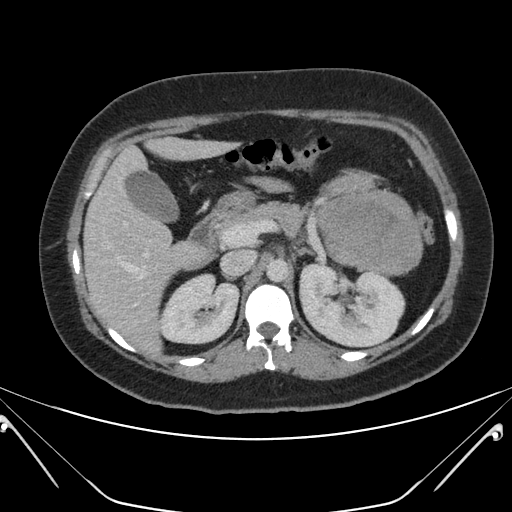
Contrast-enhanced abdominal CT, one axial slice. Intravenous contrast given. Soft-tissue window (W 400 / L 40 HU). 3 mm slice thickness. 512 × 512 image matrix, field of view 394 × 394 mm. Female patient, age 26 years. From the clinical record (not read from this slice): diagnosis: adrenocortical carcinoma; tumour side: left adrenal; tumour size at pathology: 28 cm.
Structures marked on this image (semi-automatic segmentation, software-assisted and operator-edited):
- mass: bounding box [x1, y1, x2, y2] px = [317, 173, 421, 272]